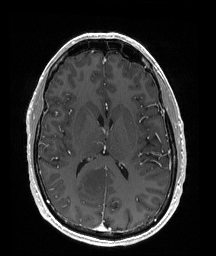
Brain MRI from a brain-tumour surgery series, one axial slice; position 87 of 176 along the scan axis; T1-weighted post-contrast; 1 mm slice thickness; 216 × 256 image matrix, field of view 211 × 250 mm. Case-level facts recorded for this patient, not image findings: histopathology: Oligodendroglioma; WHO grade: 2.
Annotated regions visible in this slice (outlined manually by an expert reader):
- tumour: box from (x=70, y=163) to (x=111, y=202) px